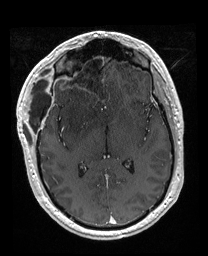
Brain MRI from a brain-tumour surgery series, one axial slice; slice 96 of 176 in the series (ordered by position); T1-weighted post-contrast; 1 mm slice thickness; 208 × 256 image matrix, field of view 208 × 256 mm. Case-level facts recorded for this patient, not image findings: histopathology: Astrocytoma; WHO grade: 4; IDH mutation: yes.
Structures marked on this image (expert manual segmentation):
- previous resection cavity: bounding box [x1, y1, x2, y2] px = [56, 52, 106, 88]